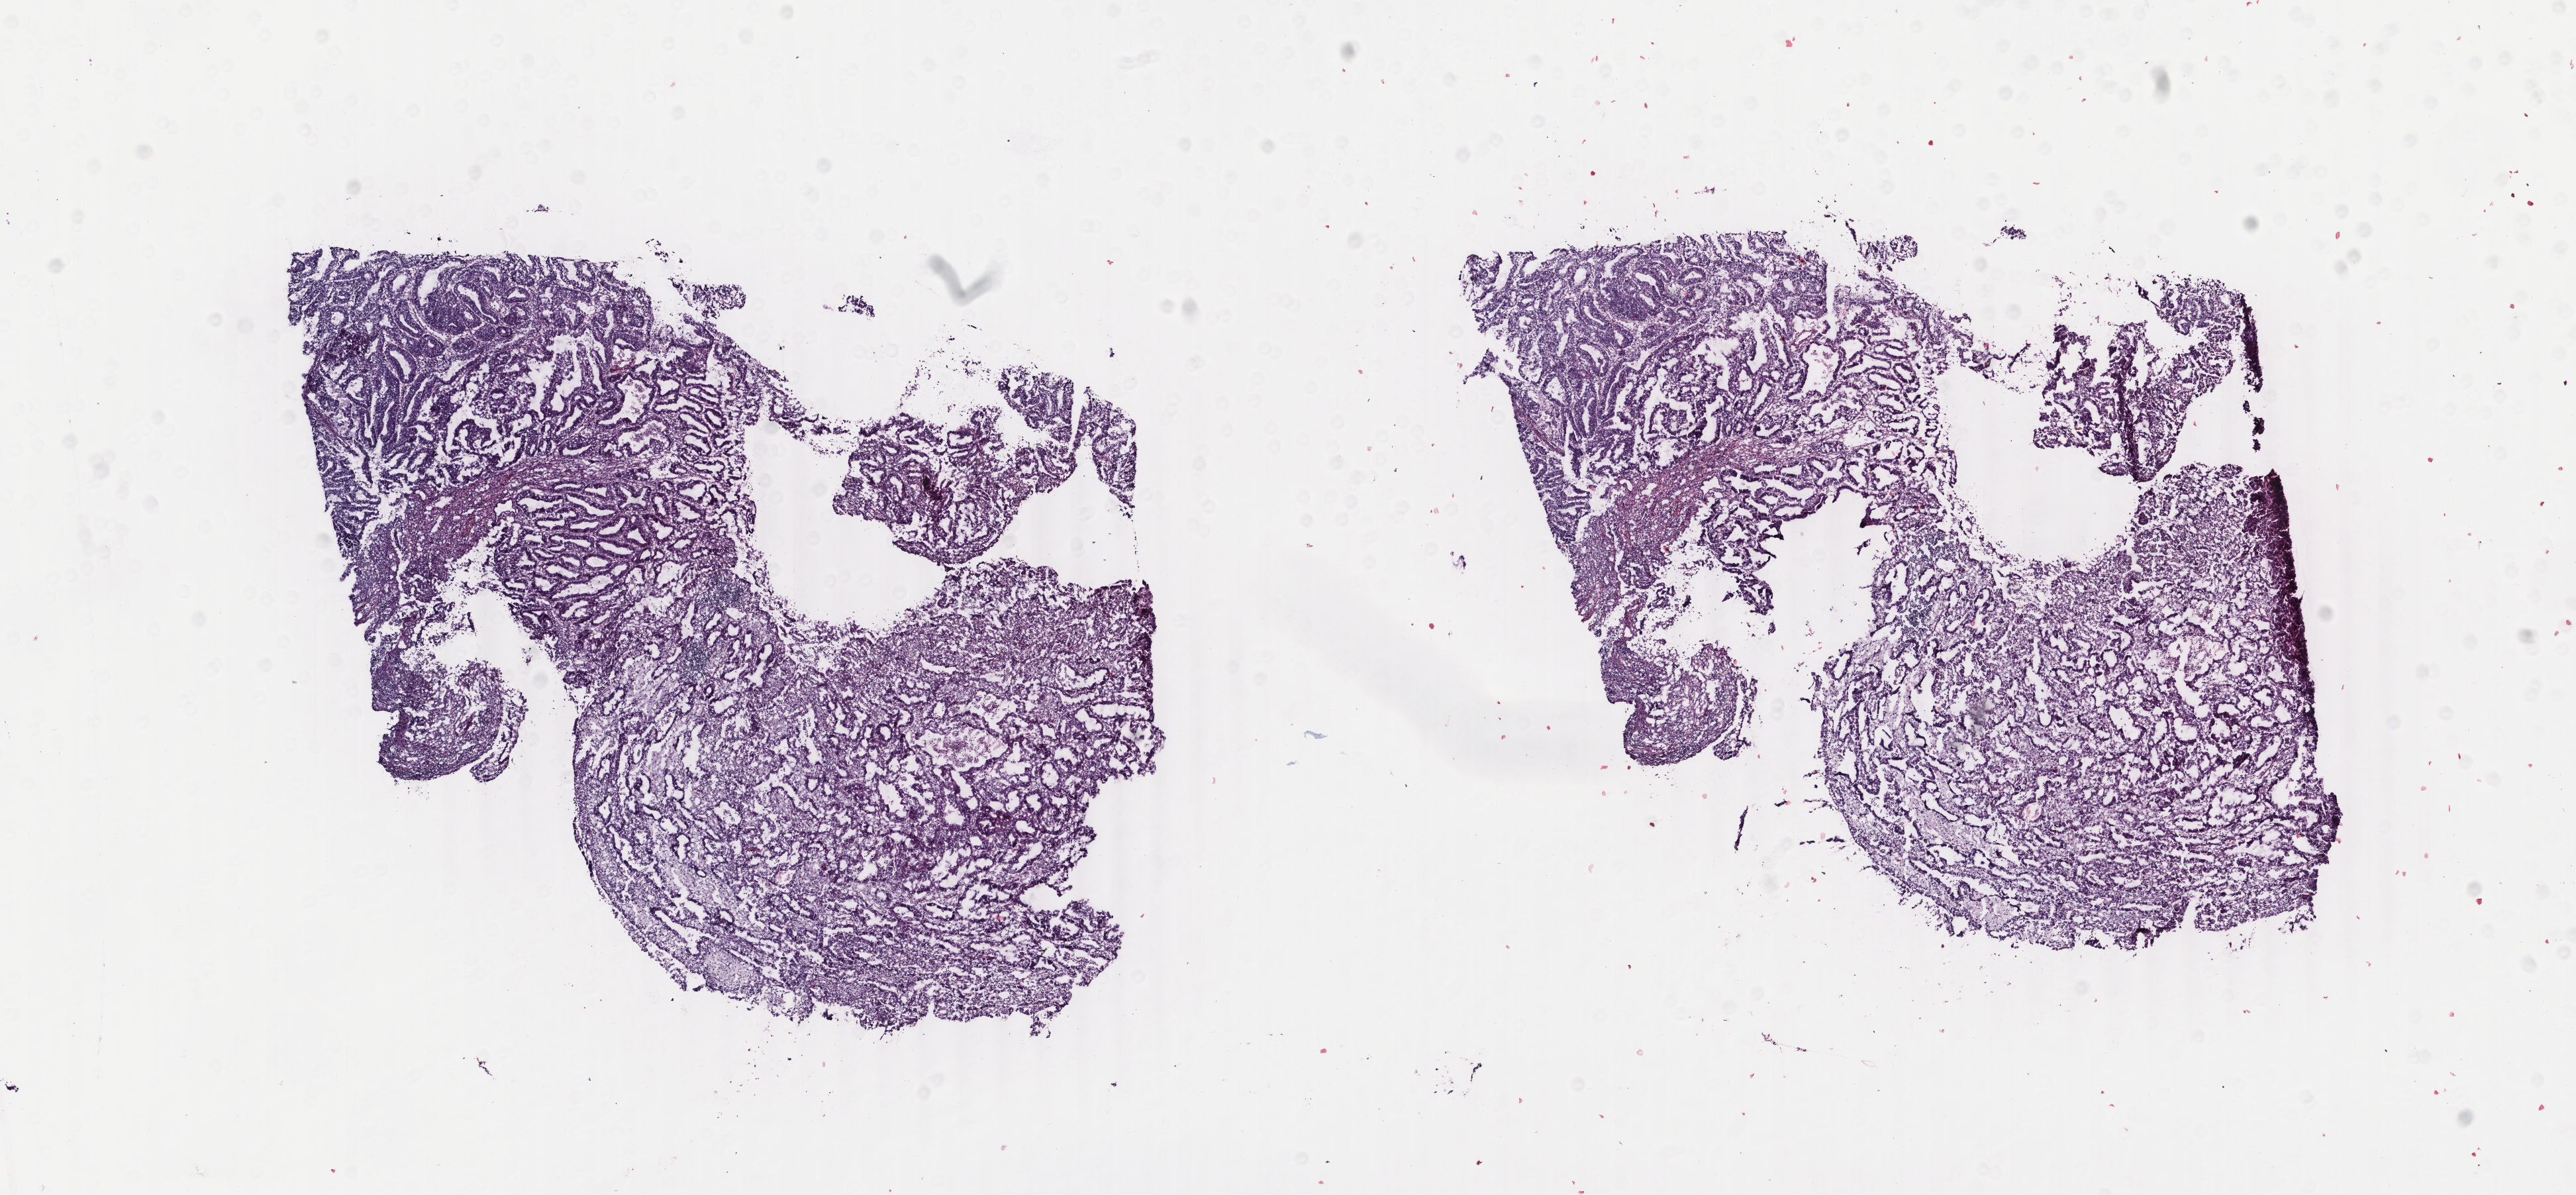
Whole-slide histology image, Hematoxylin and eosin (H&E) stained, a low-resolution overview of the entire scanned area, about 15.5 x 7.2 mm (slide scanned at 40x); frozen section; sample: primary tumour, uterus. Female, age 76 years at initial diagnosis. Histologic grade: G1 (well differentiated). Pathologist review of this section (percent, as recorded): tumour cells 5%, tumour nuclei 2%, normal cells 0%, stromal cells 92%, necrosis 3%. Infiltration values recorded for this section: lymphocyte infiltration 20%, monocyte infiltration 5%, neutrophil infiltration 30%.
• pathologic diagnosis: Endometrioid adenocarcinoma, NOS (endometrium)
• FIGO stage: IB